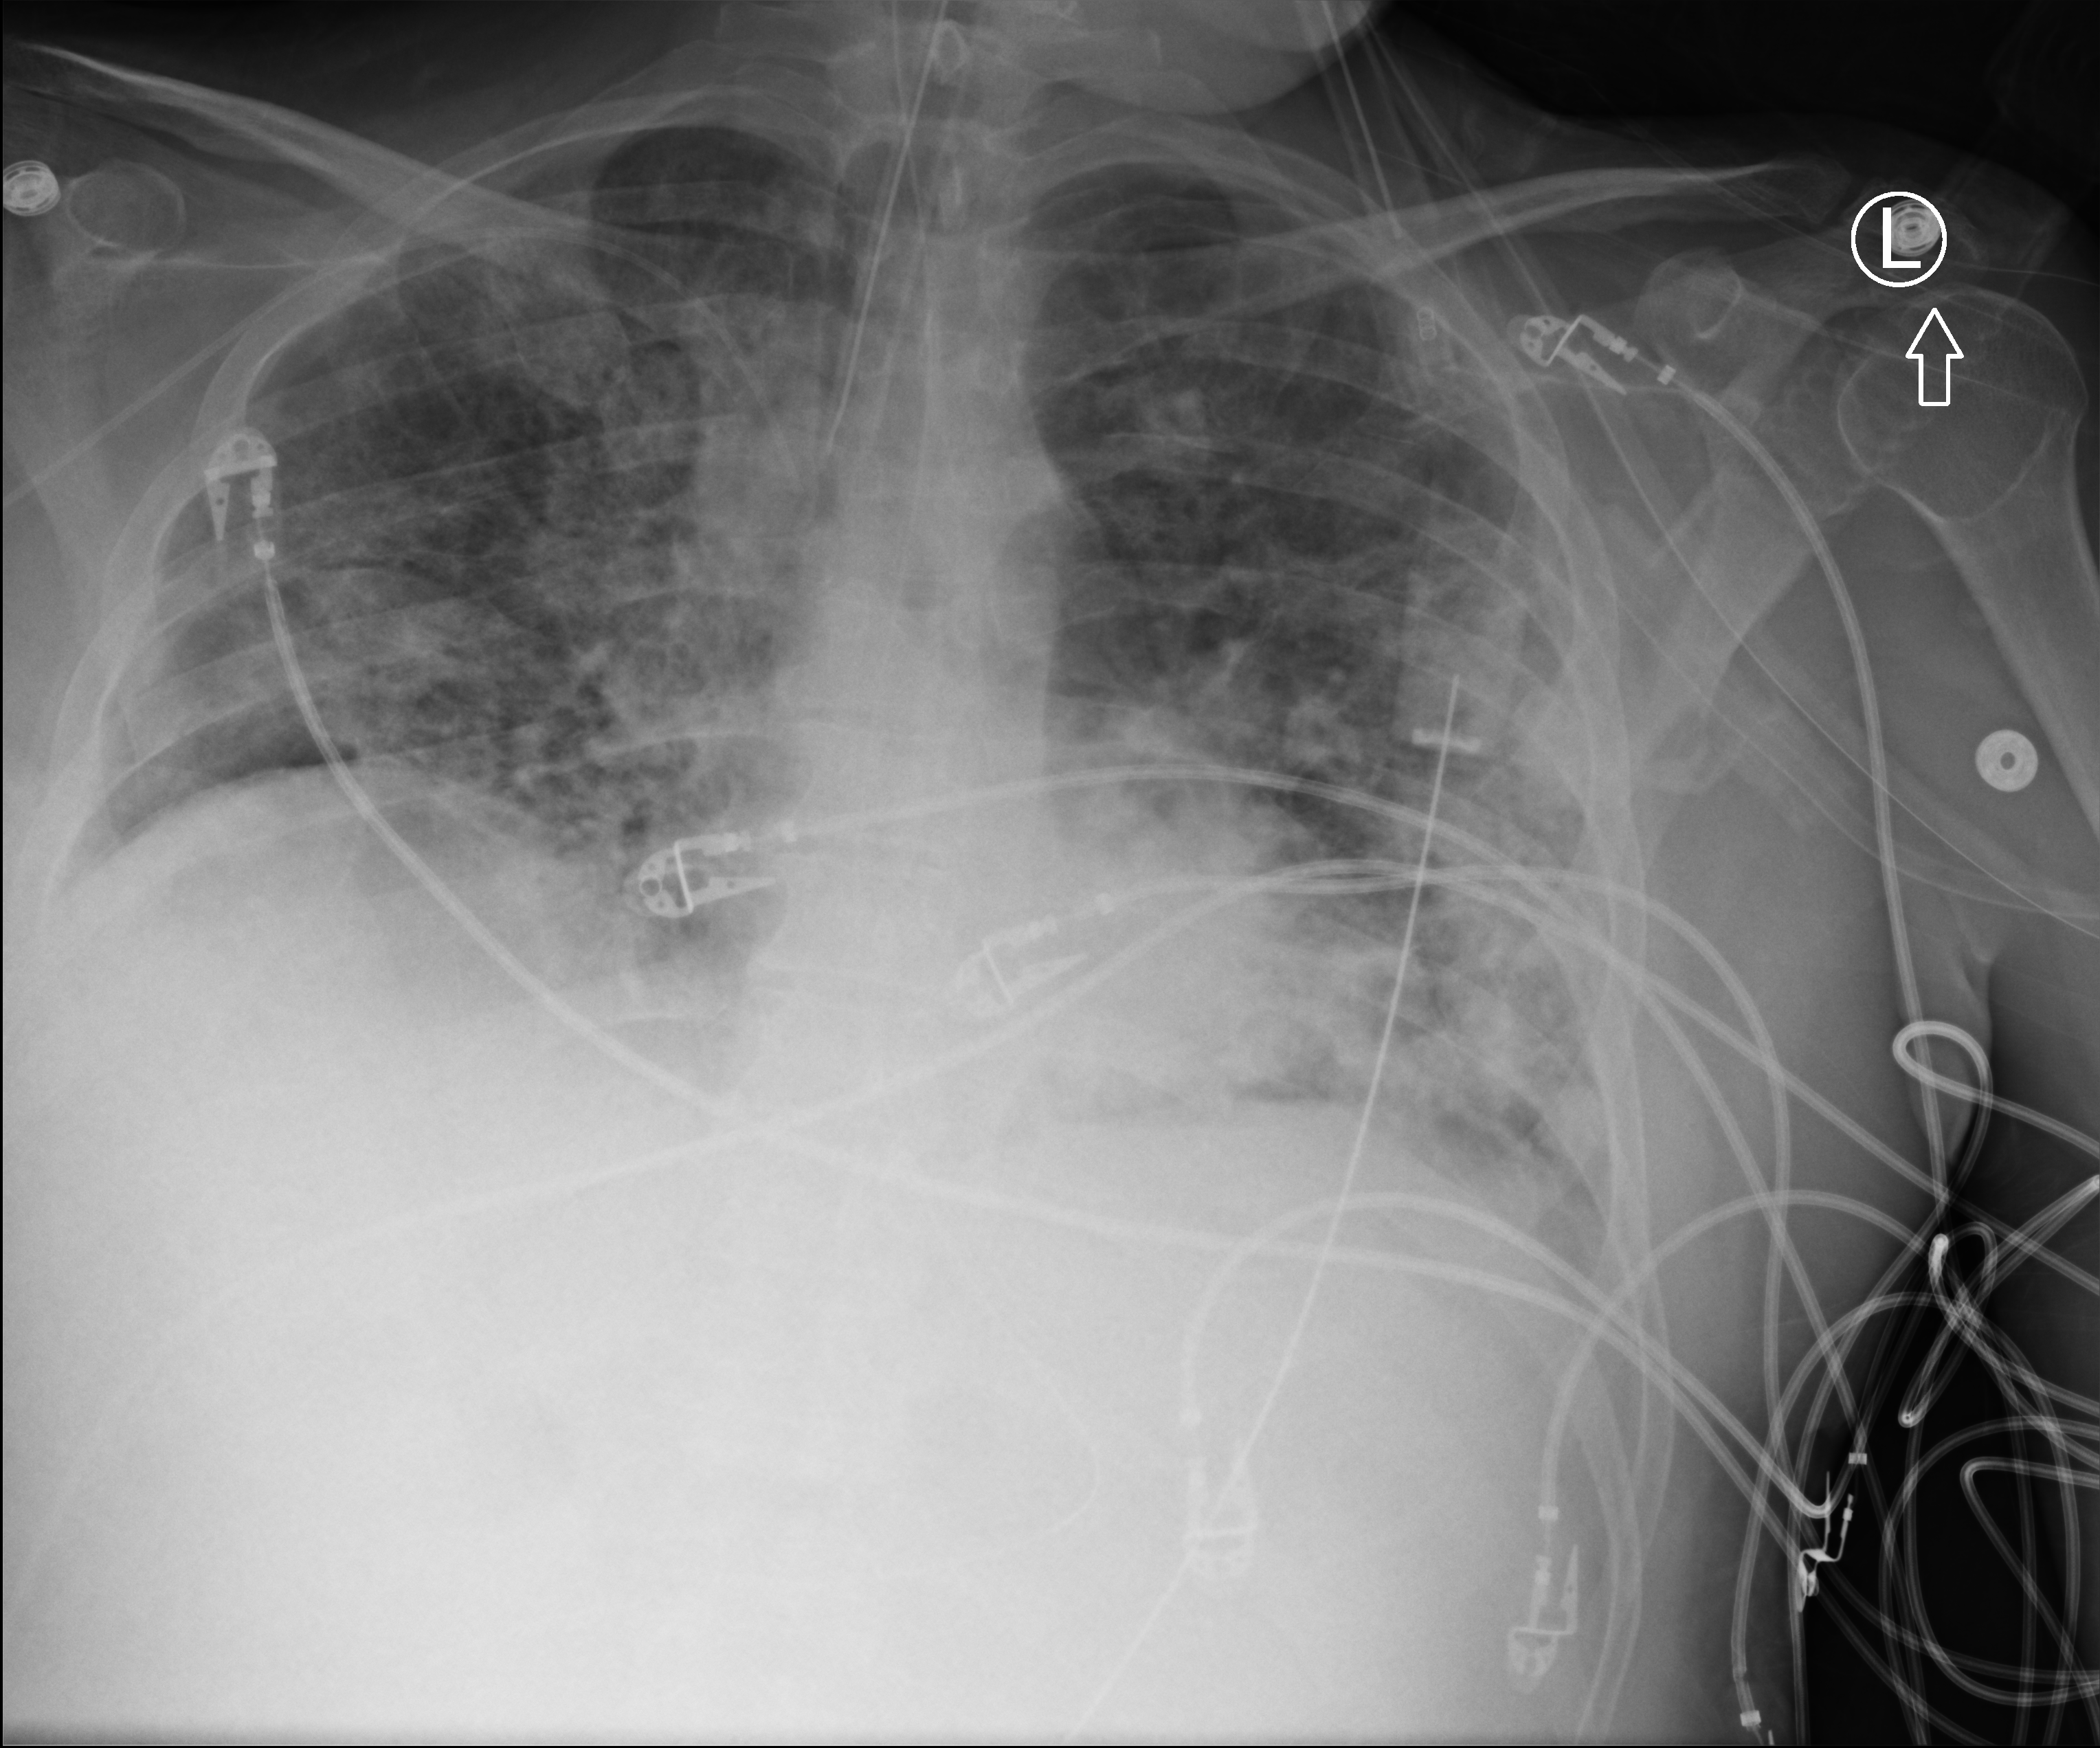
Portable chest radiograph, anteroposterior (AP) projection. Male patient hospitalised with COVID-19, age 18–59 years.
Hospital-stay facts (about this admission, not read from this image; timing relative to this image not recorded):
- admitted to intensive care during this hospital stay: yes
- chronic kidney disease (admission record): no
- diabetes (admission record): no